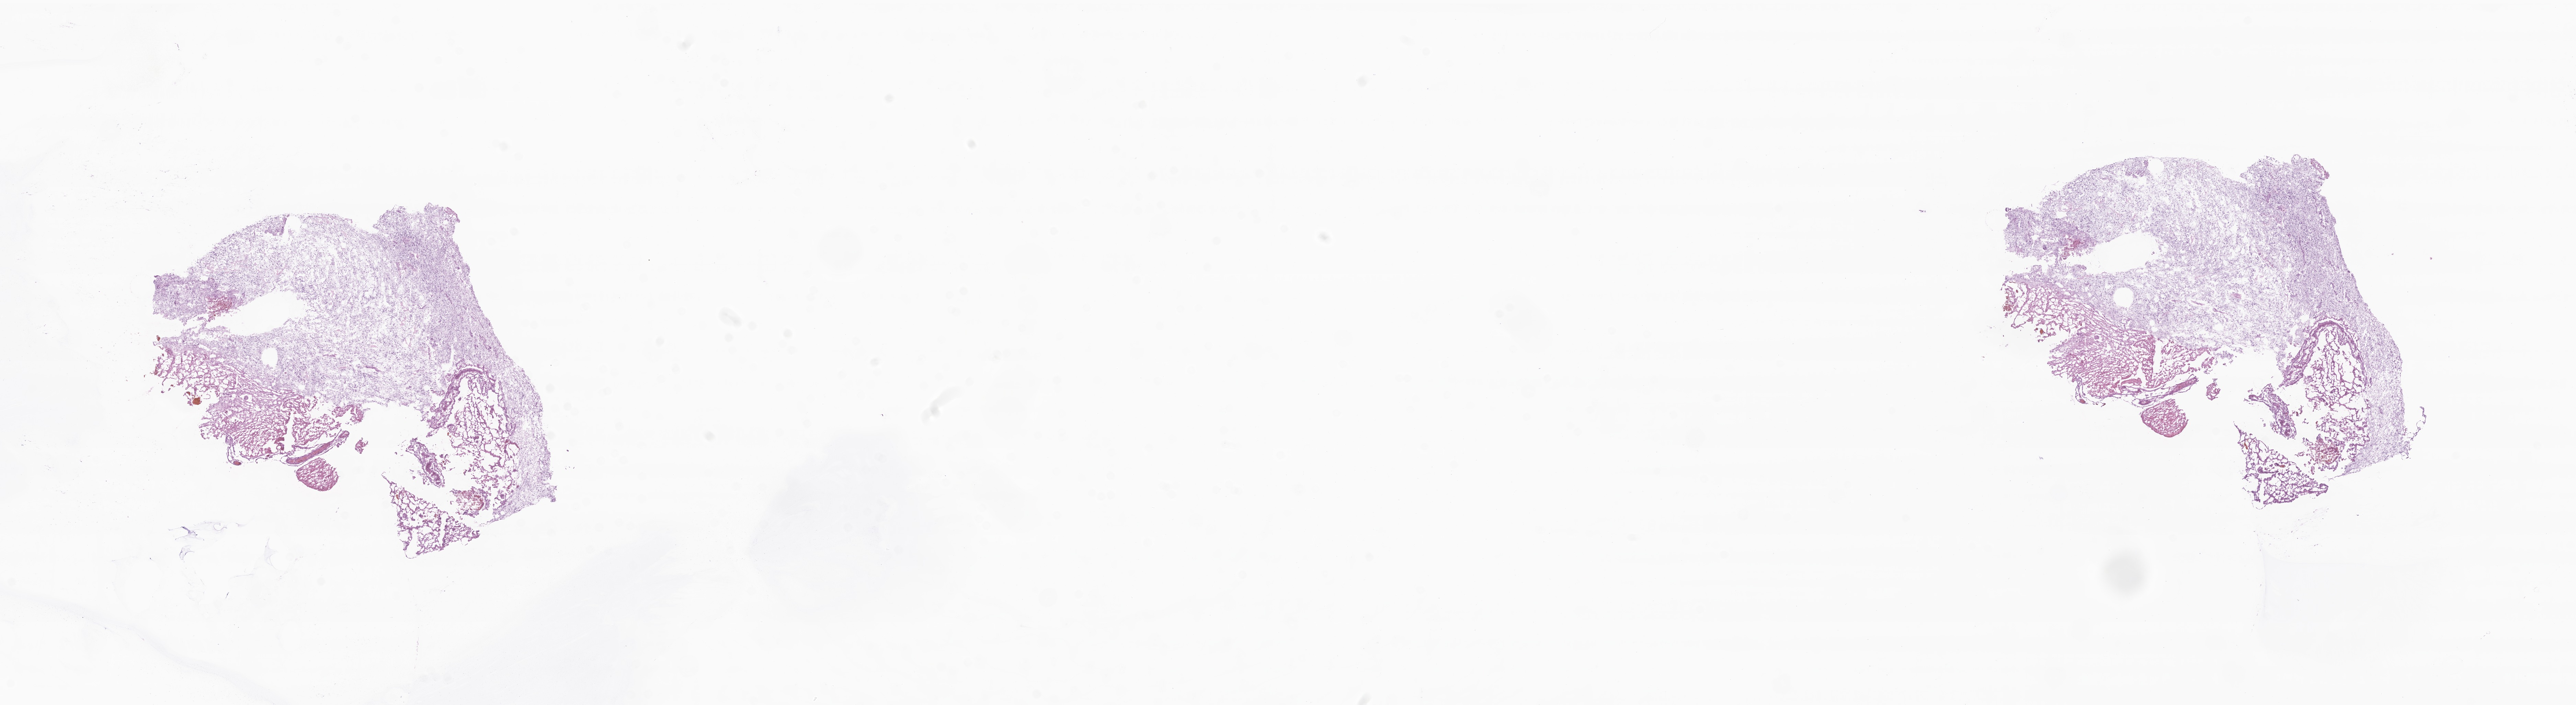
H&E whole-slide image of tumor tissue from the brain, low-resolution overview of the scanned area, about 31.6 x 8.7 mm. Cryosection (OCT / tissue freezing medium). Patient: female, age 598 days (about 1.6 years).
- diagnosis: Glioma, malignant